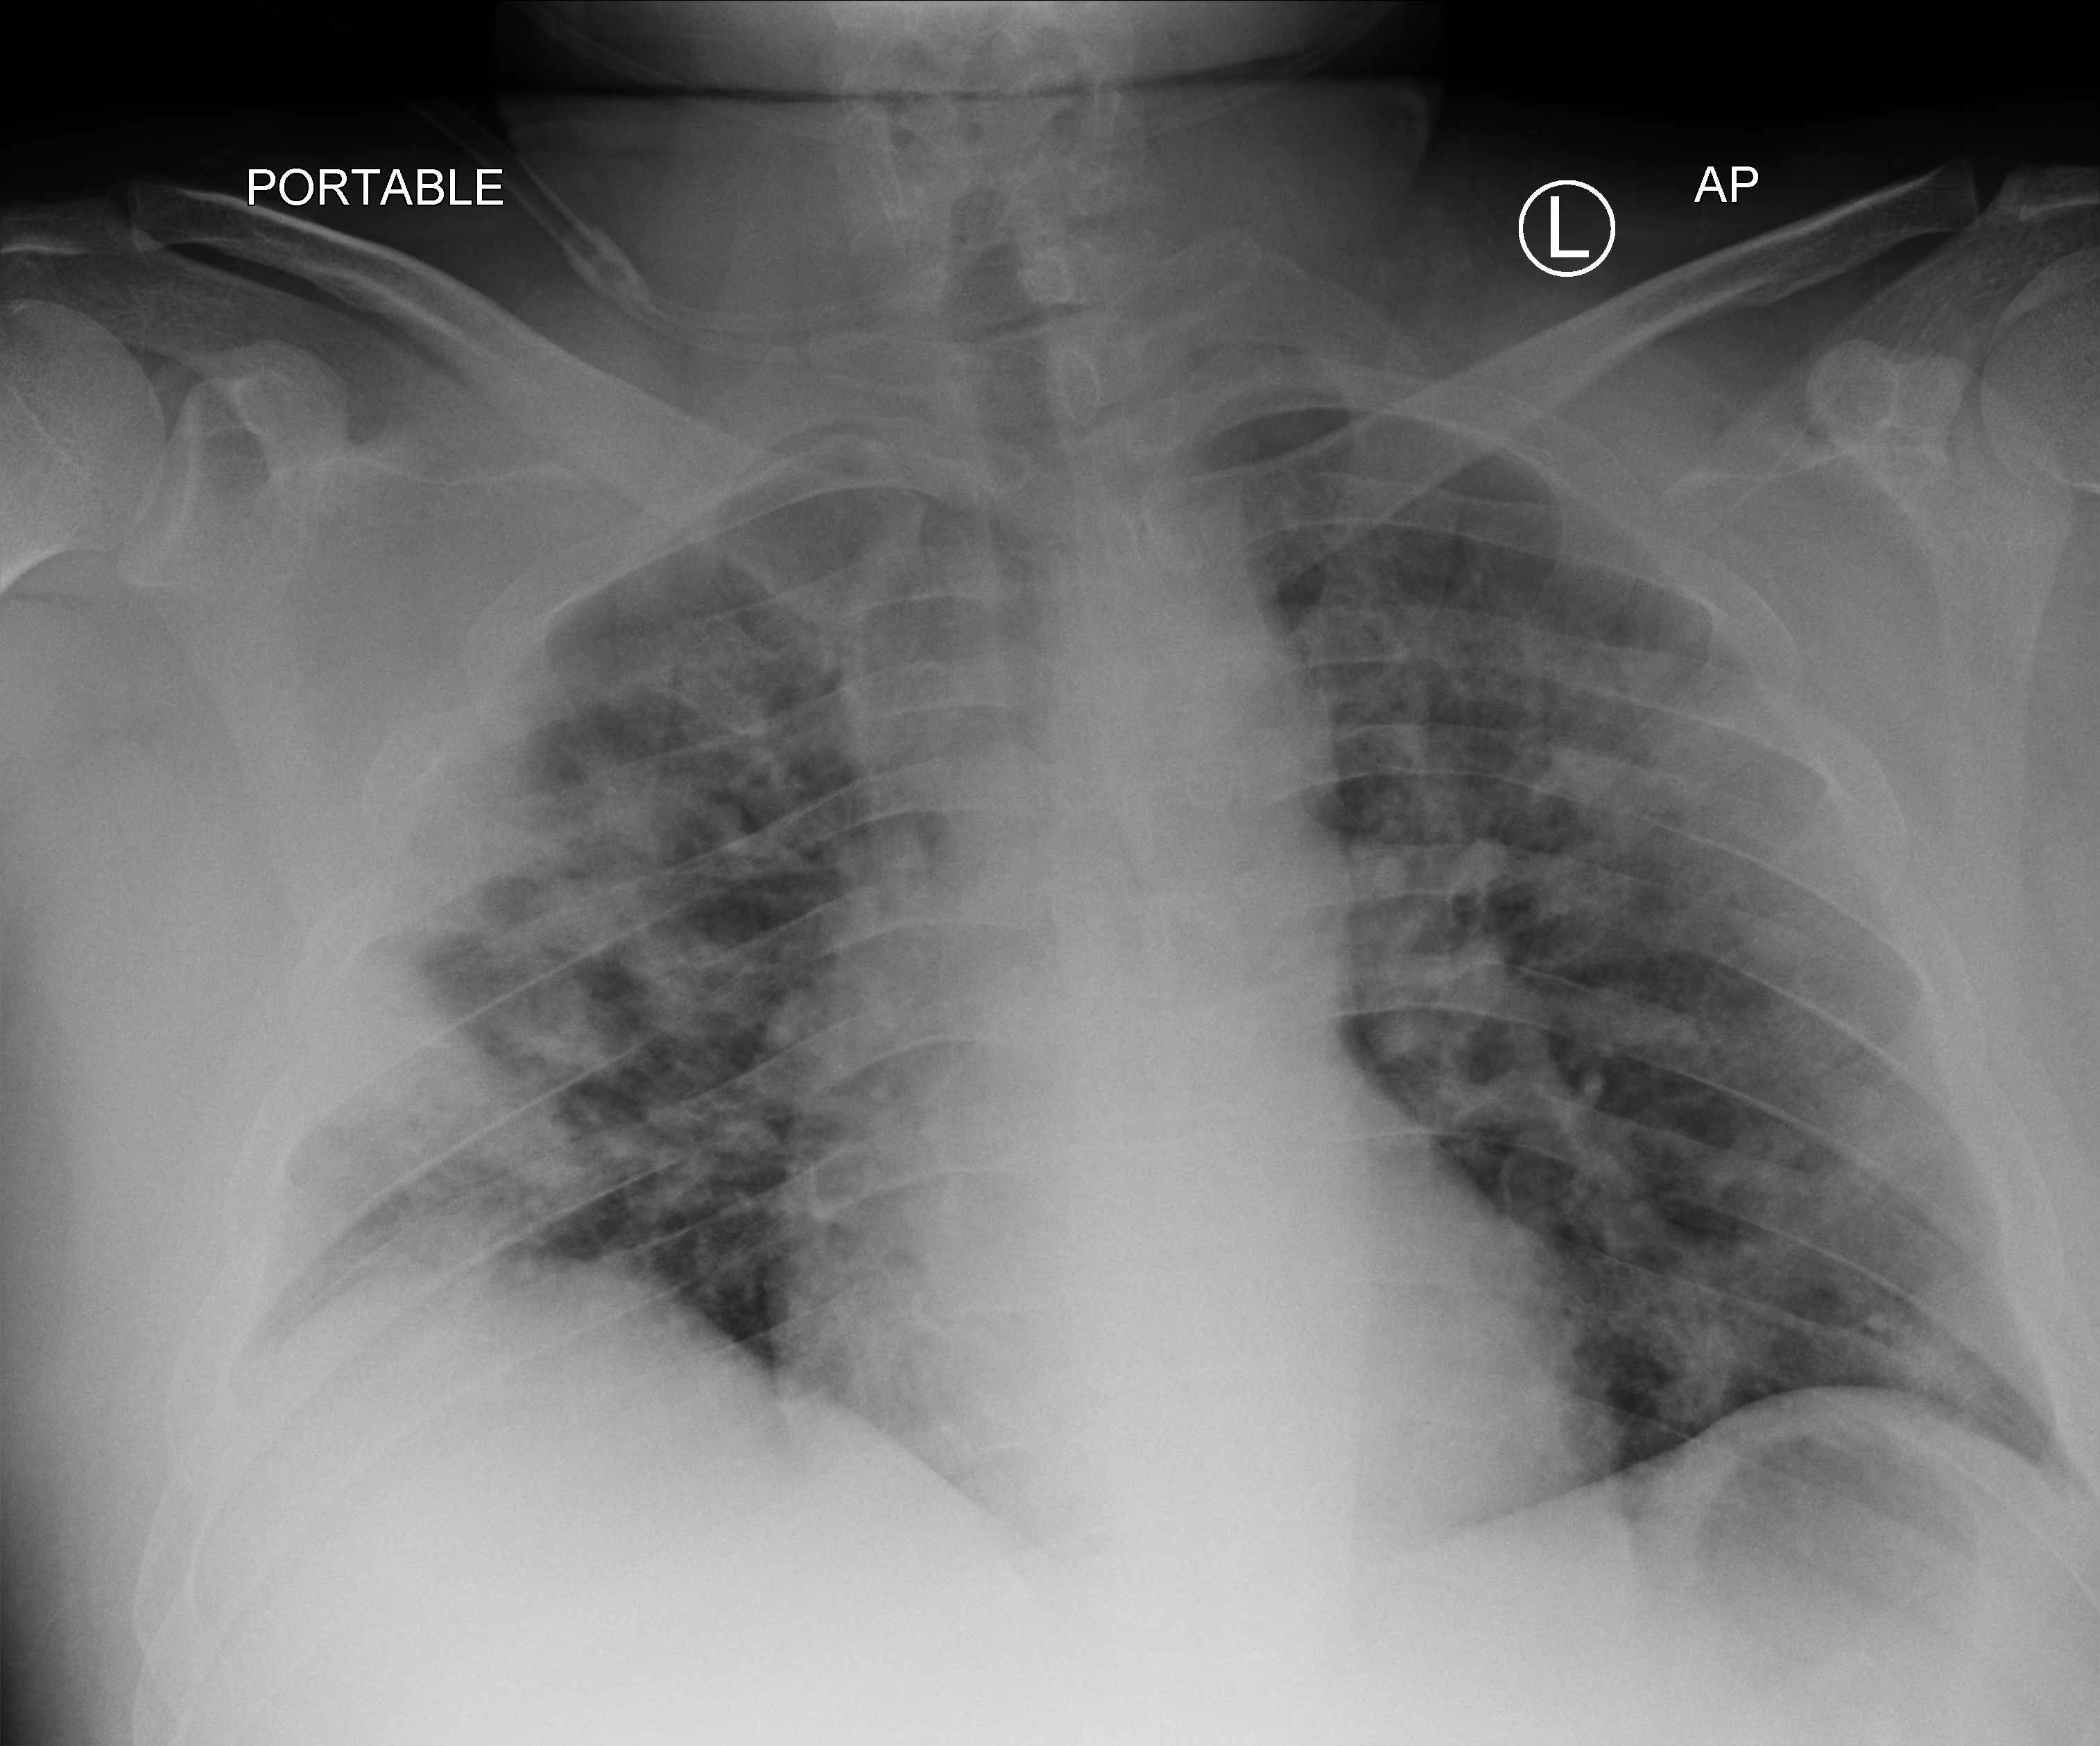
Portable chest radiograph. Female patient hospitalised with COVID-19, age 18–59 years.
Admission-level facts for this patient (not findings on this image; timing relative to this image not recorded): COPD (admission record): no; other chronic lung disease (admission record): no.